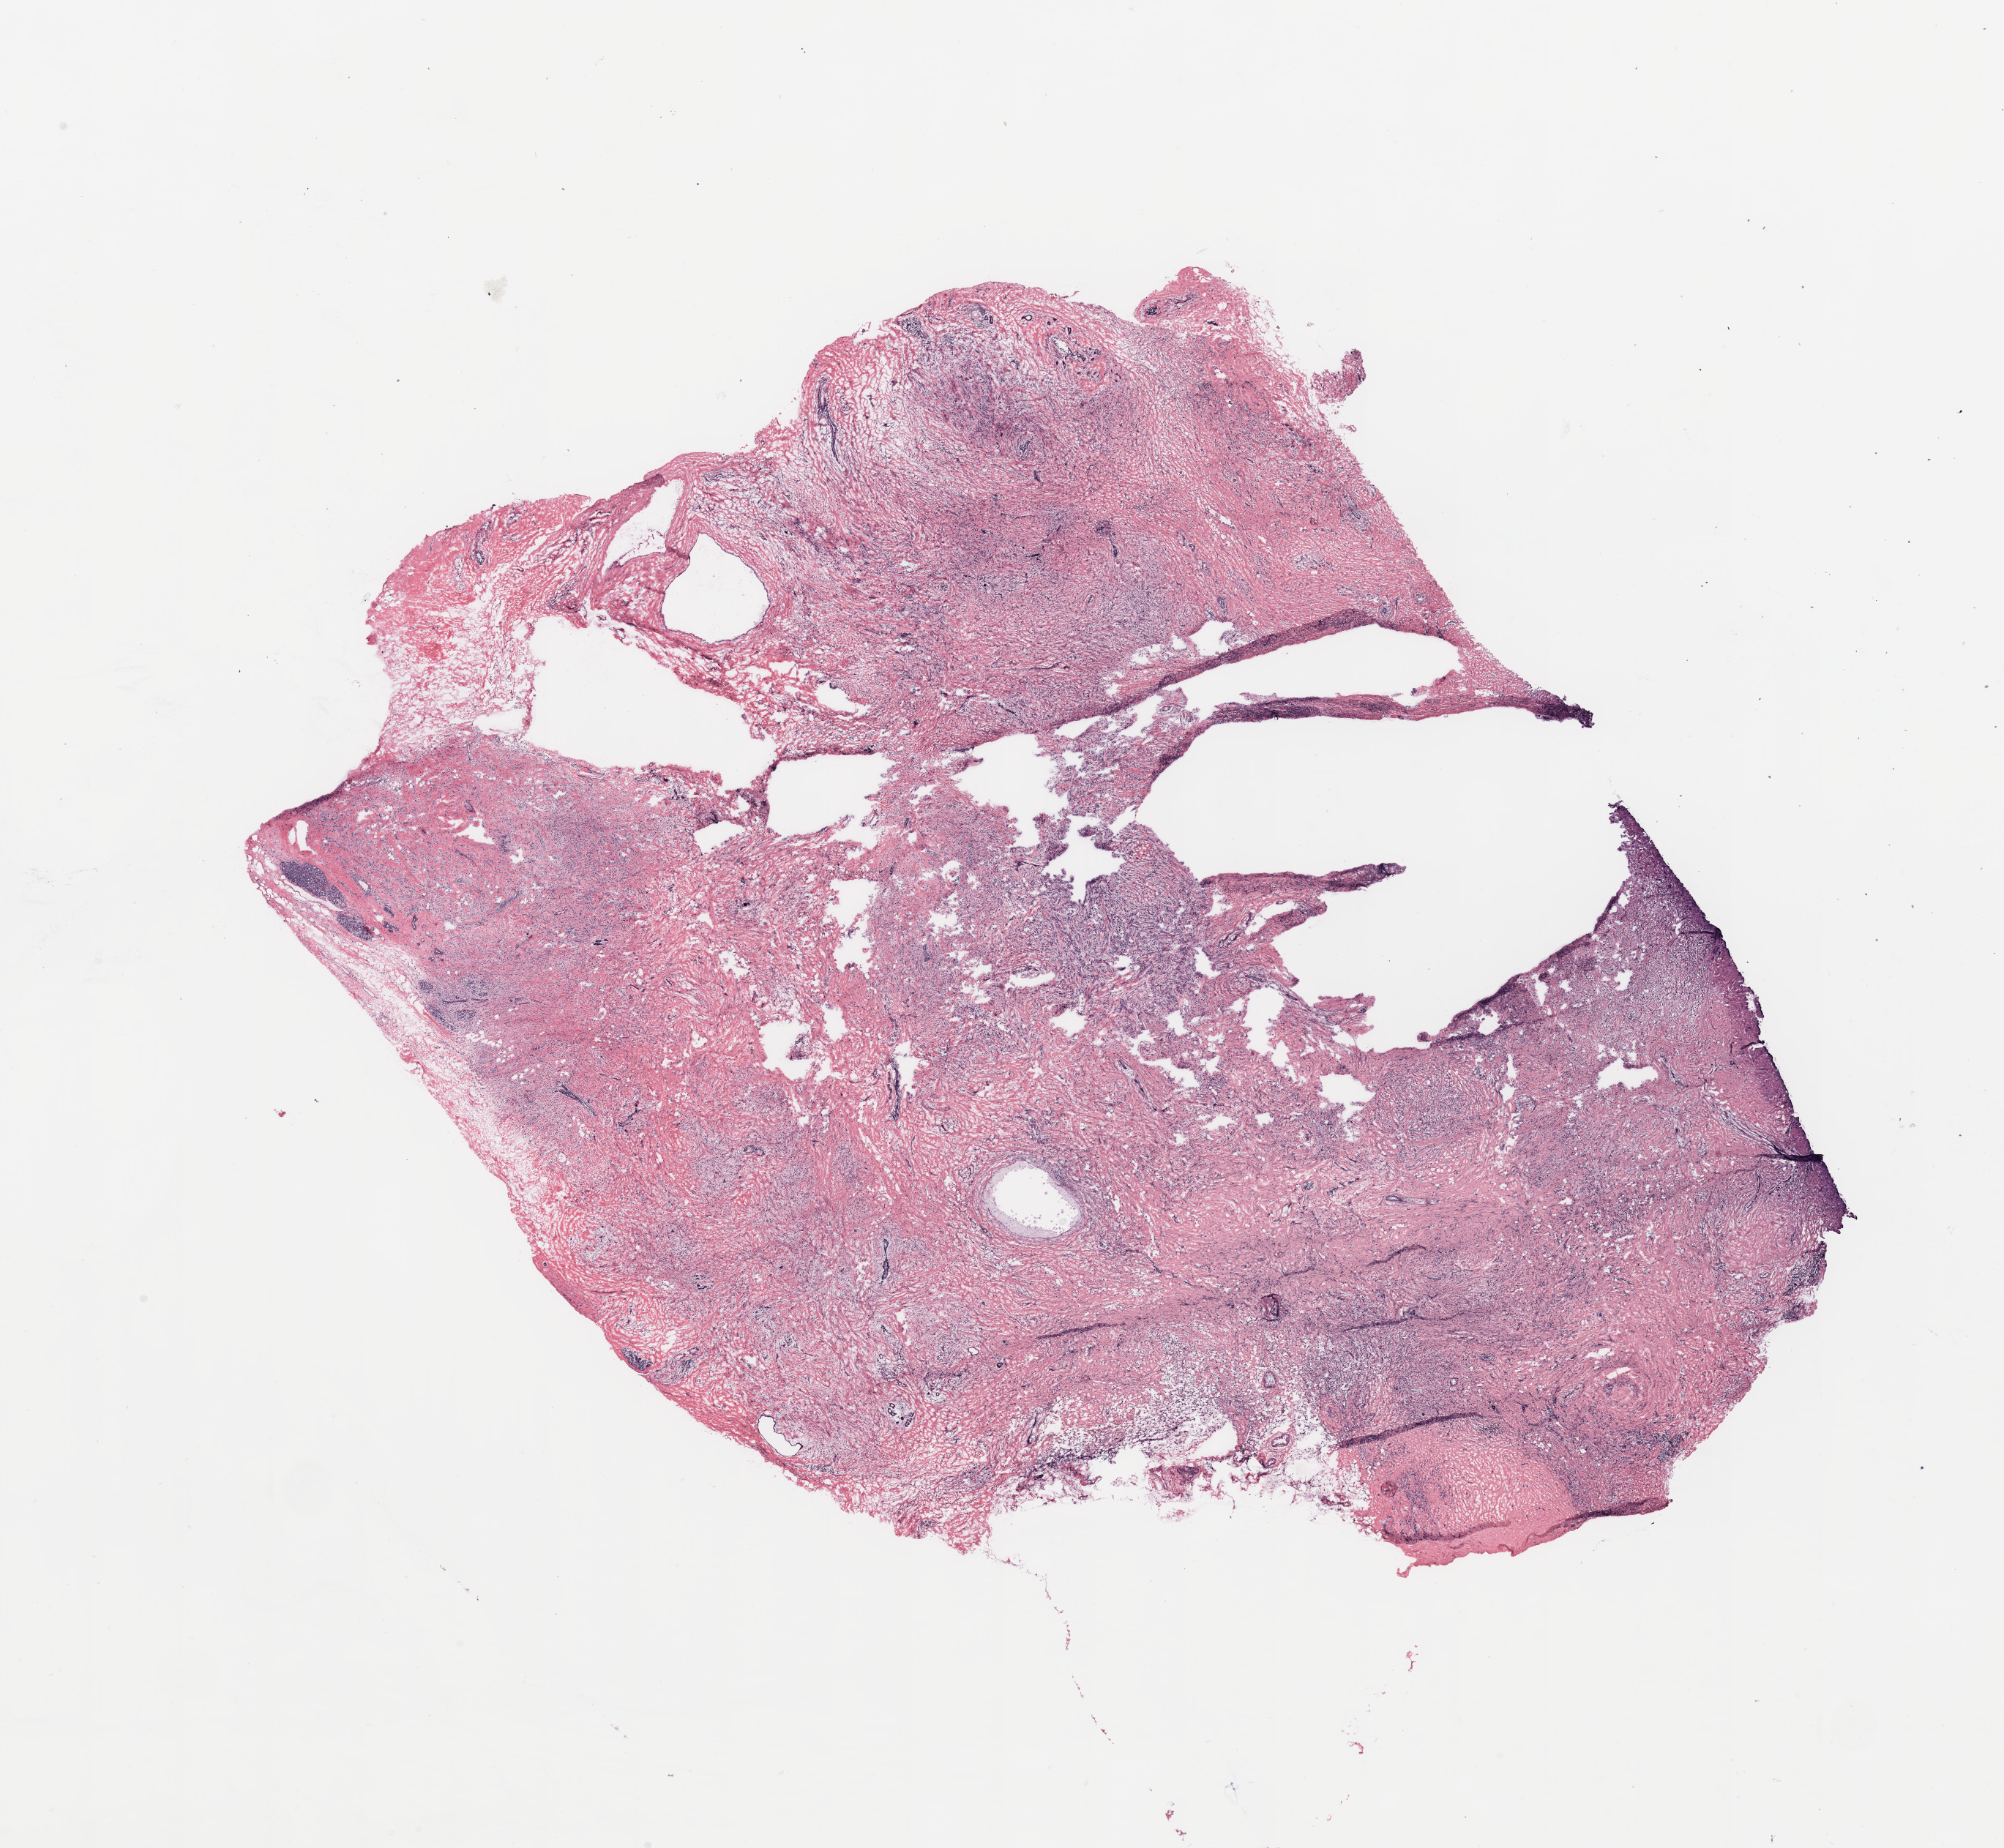
Whole-slide histology image, Hematoxylin and eosin (H&E) stained — whole scanned area (about 21.7 x 20.0 mm) shown as a low-resolution overview, breast, tissue type not recorded.
Patient diagnosis (cohort enrolment): breast cancer (breast).